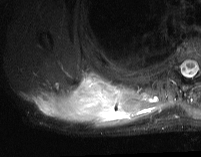
MRI of an extremity soft-tissue mass, one axial slice; slice 22 of 74 in the series (ordered by position); STIR; MR volume resampled by the dataset authors to the PET/CT grid (not the native acquisition matrix); 3.27 mm slice thickness; 201 × 157 image matrix, field of view 196 × 153 mm. Male patient. Case-level facts recorded for this patient, not image findings: histological type: pleiomorphic spindle cell undifferentiated; grade: high; site of the primary tumour: right parascapusular.
Annotated regions visible in this slice (expert contour drawn on MRI and transferred to this co-registered scan by the dataset authors):
- gross tumour volume including surrounding oedema: bounding box <28,73,162,129> (left, top, right, bottom; pixels)
- gross tumour volume (mass): <40,75,125,124>